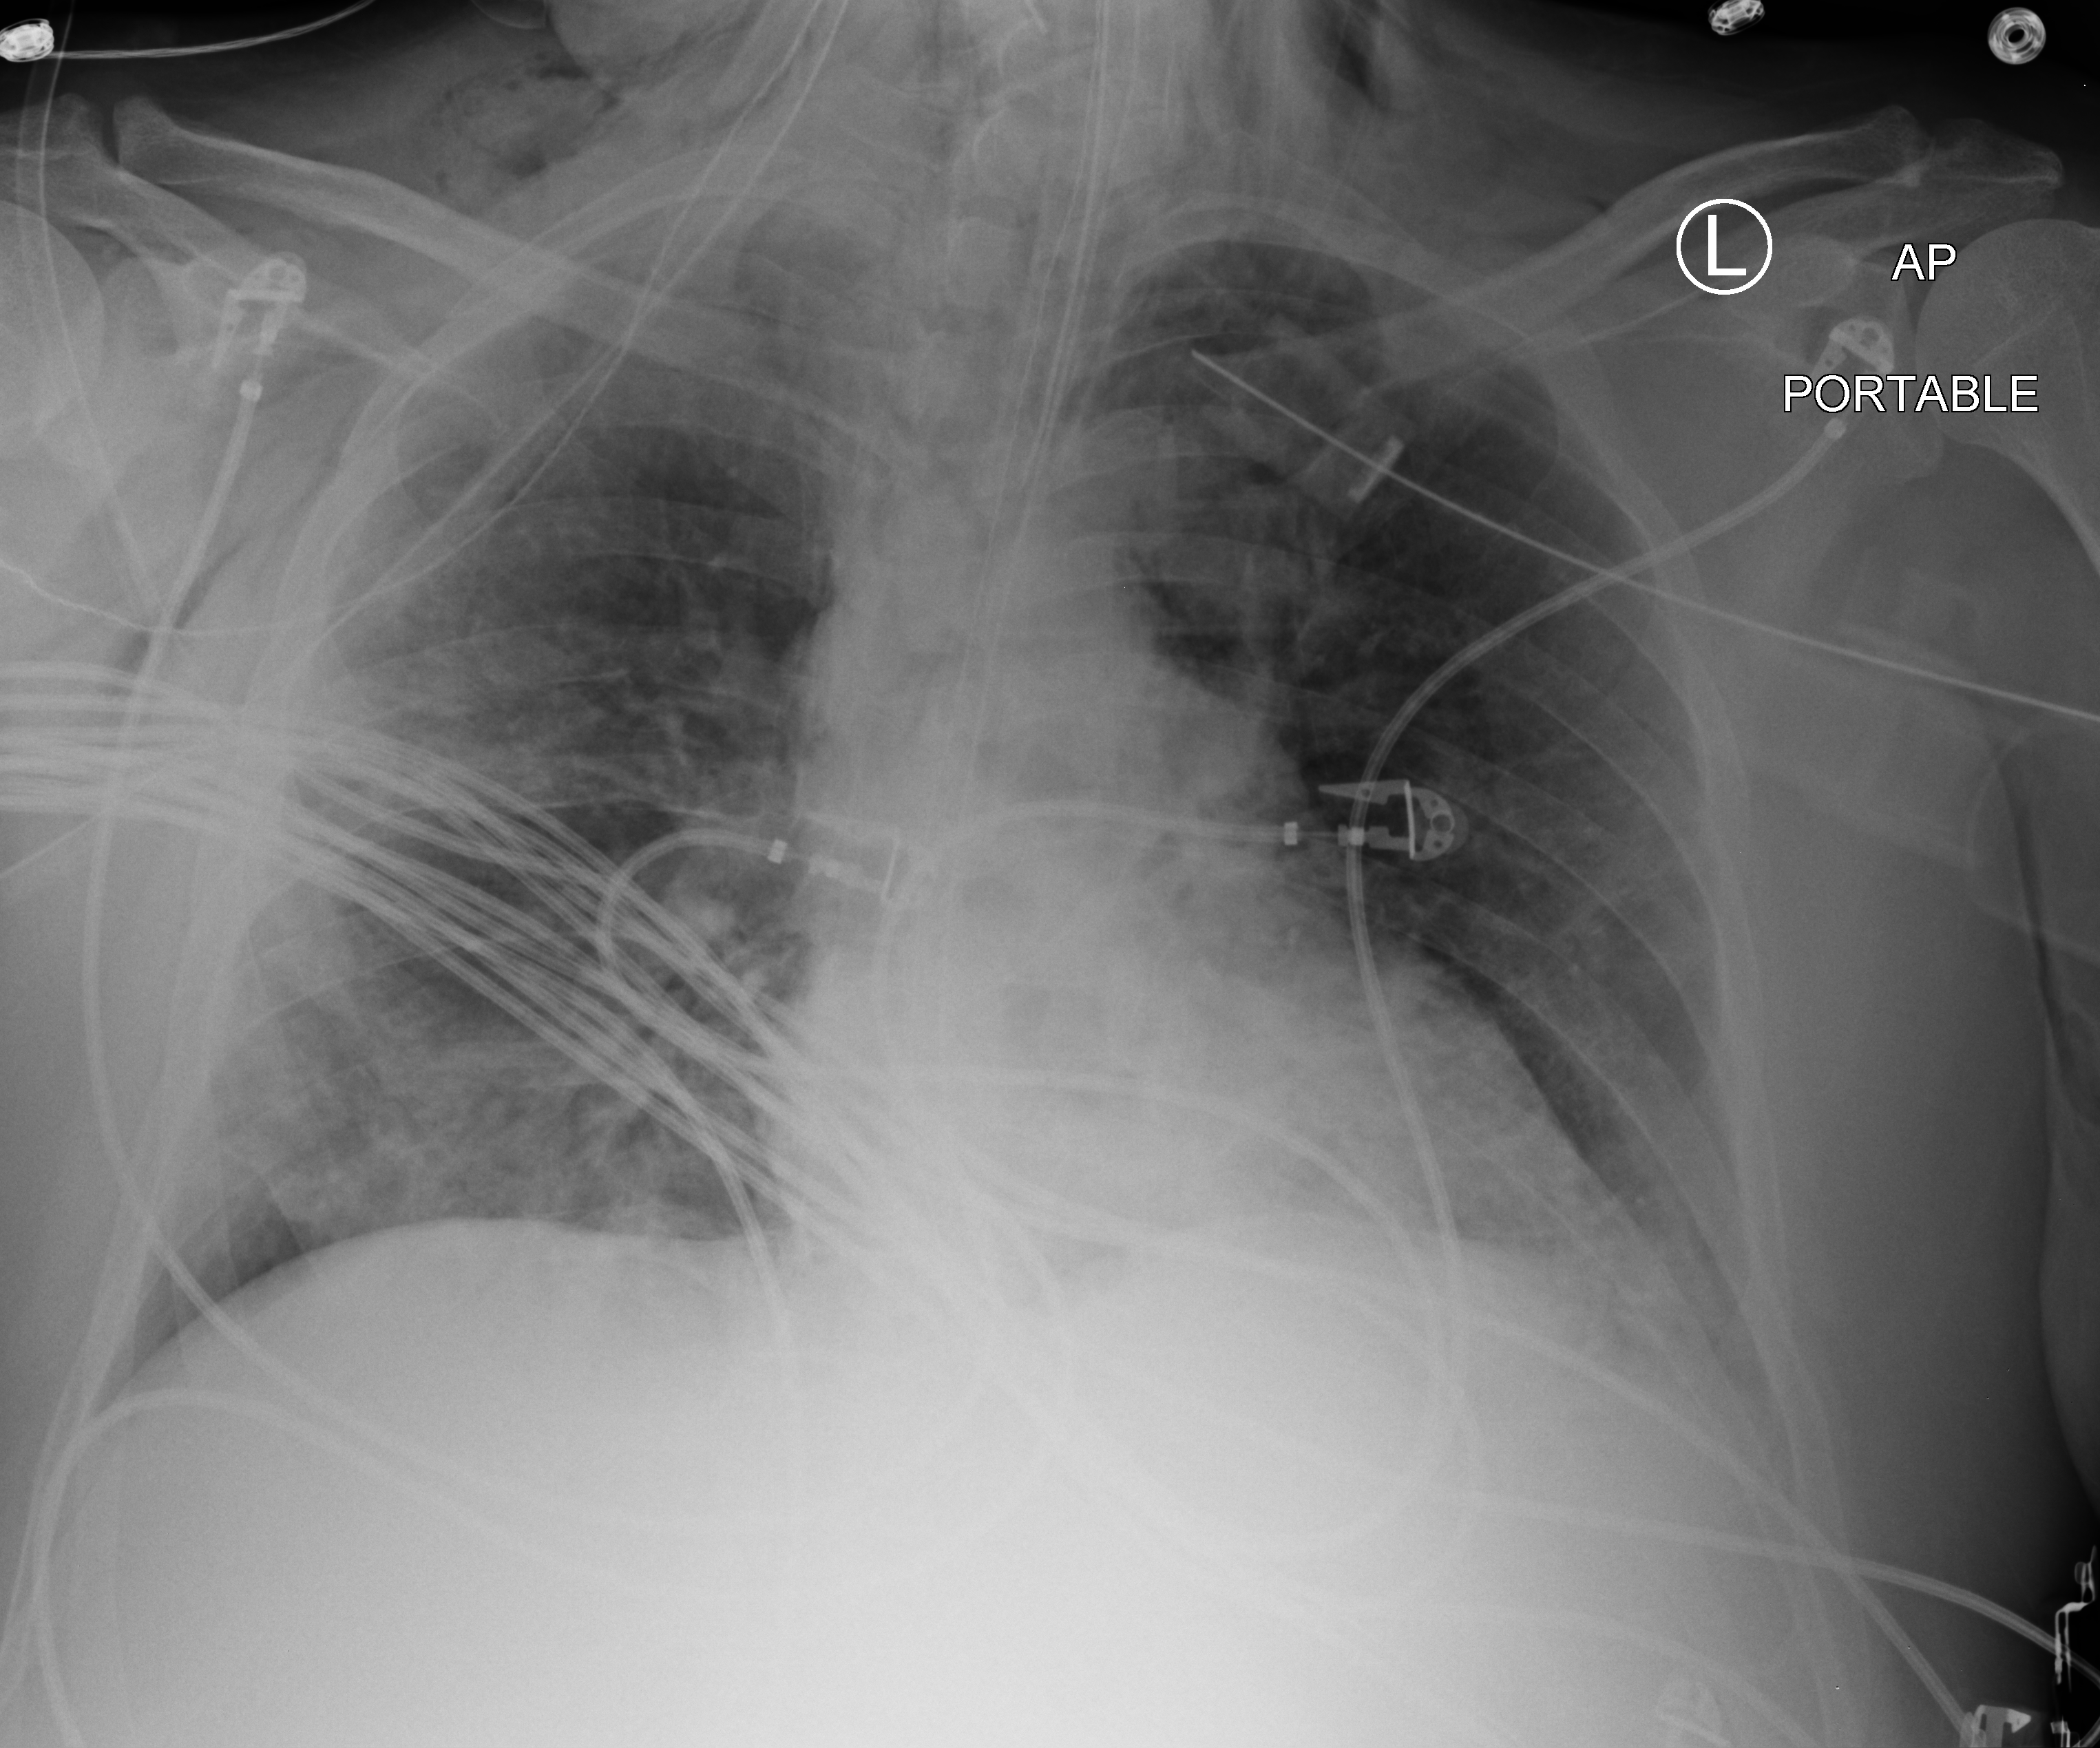
Portable chest radiograph; anteroposterior (AP) projection. Patient hospitalised with COVID-19, aged 18–59 years.
Admission-level facts for this patient (not findings on this image; timing relative to this image not recorded):
- admitted to intensive care during this hospital stay: yes
- mechanically ventilated during this hospital stay: yes